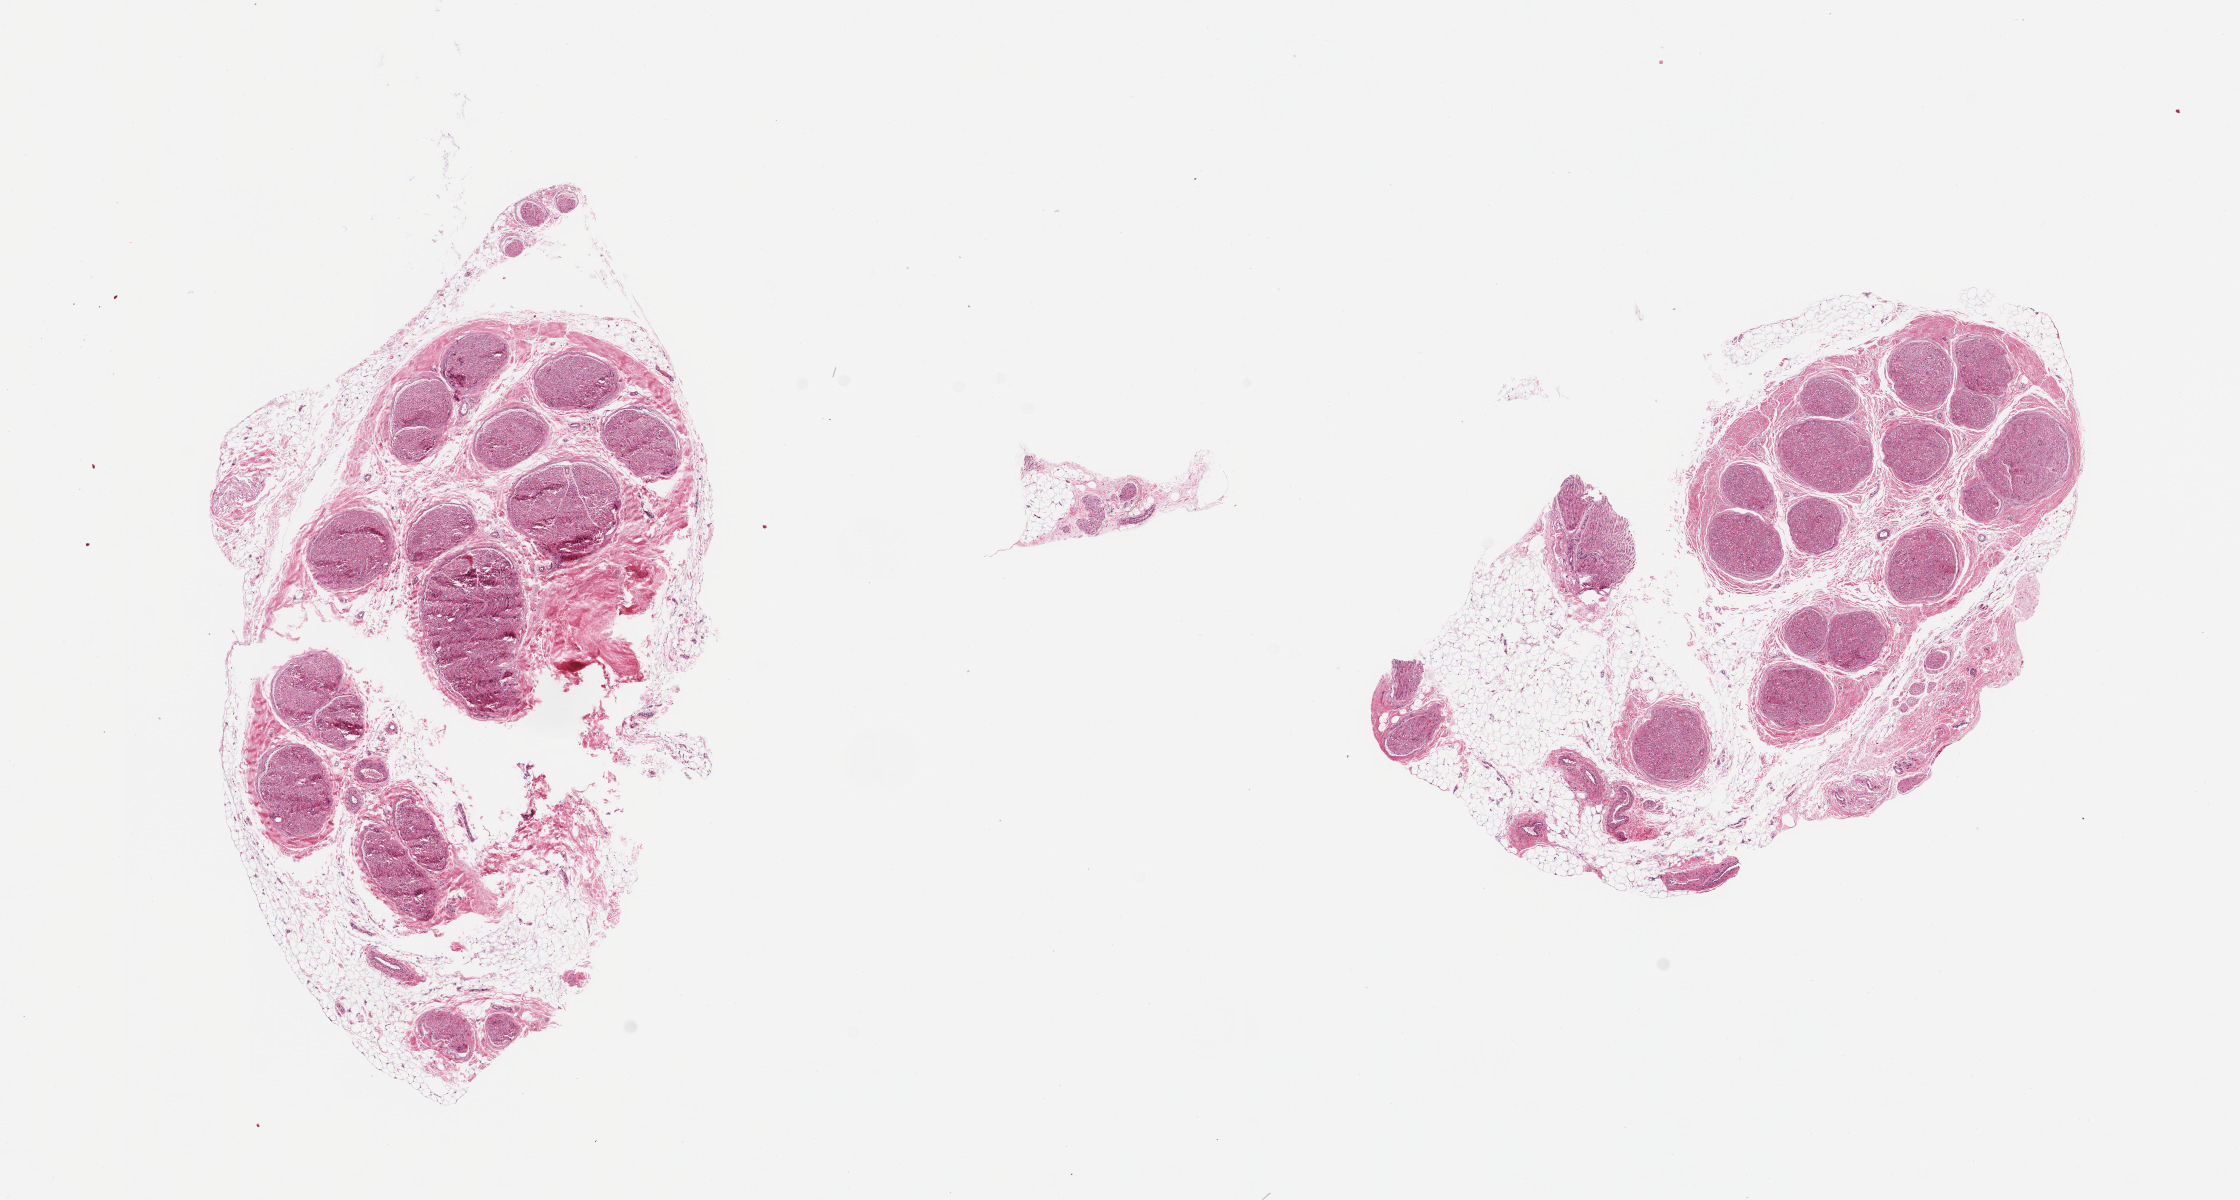
Whole-slide image, haematoxylin and eosin stain, a low-resolution overview of the entire scanned area, about 17.7 x 9.5 mm (from a 20x scan); PAXgene-fixed, paraffin-embedded tissue; target tissue: tibial nerve; tissue donor sample. Donor sex: female.
Reviewer comment on this tissue sample: 2 pieces, focal adherent fat up to ~0.6mm.